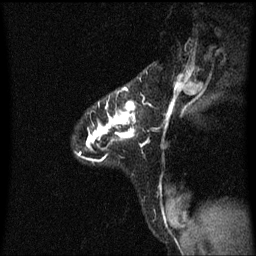
Breast MRI (dynamic contrast-enhanced), one sagittal slice; position 47 of 60 along the scan axis; dynamic contrast-enhanced series, image 2 of 3 at this slice position (ordered by acquisition); 1.5 T; TE 4.2 ms, TR 8.4 ms; 2 mm slice thickness; 256 × 256 image matrix, field of view 200 × 200 mm. Patient: female, 32 years.
Annotated regions visible in this slice (semi-automatically segmented with operator editing):
- analysis volume of interest (the breast-tissue region the enhancement analysis was run in; not a lesion): bounding box [x1, y1, x2, y2] px = [80, 86, 145, 161]
- tumour enhancement mask (voxels above the 70 % enhancement threshold inside the analysis volume of interest): [80, 88, 136, 155]